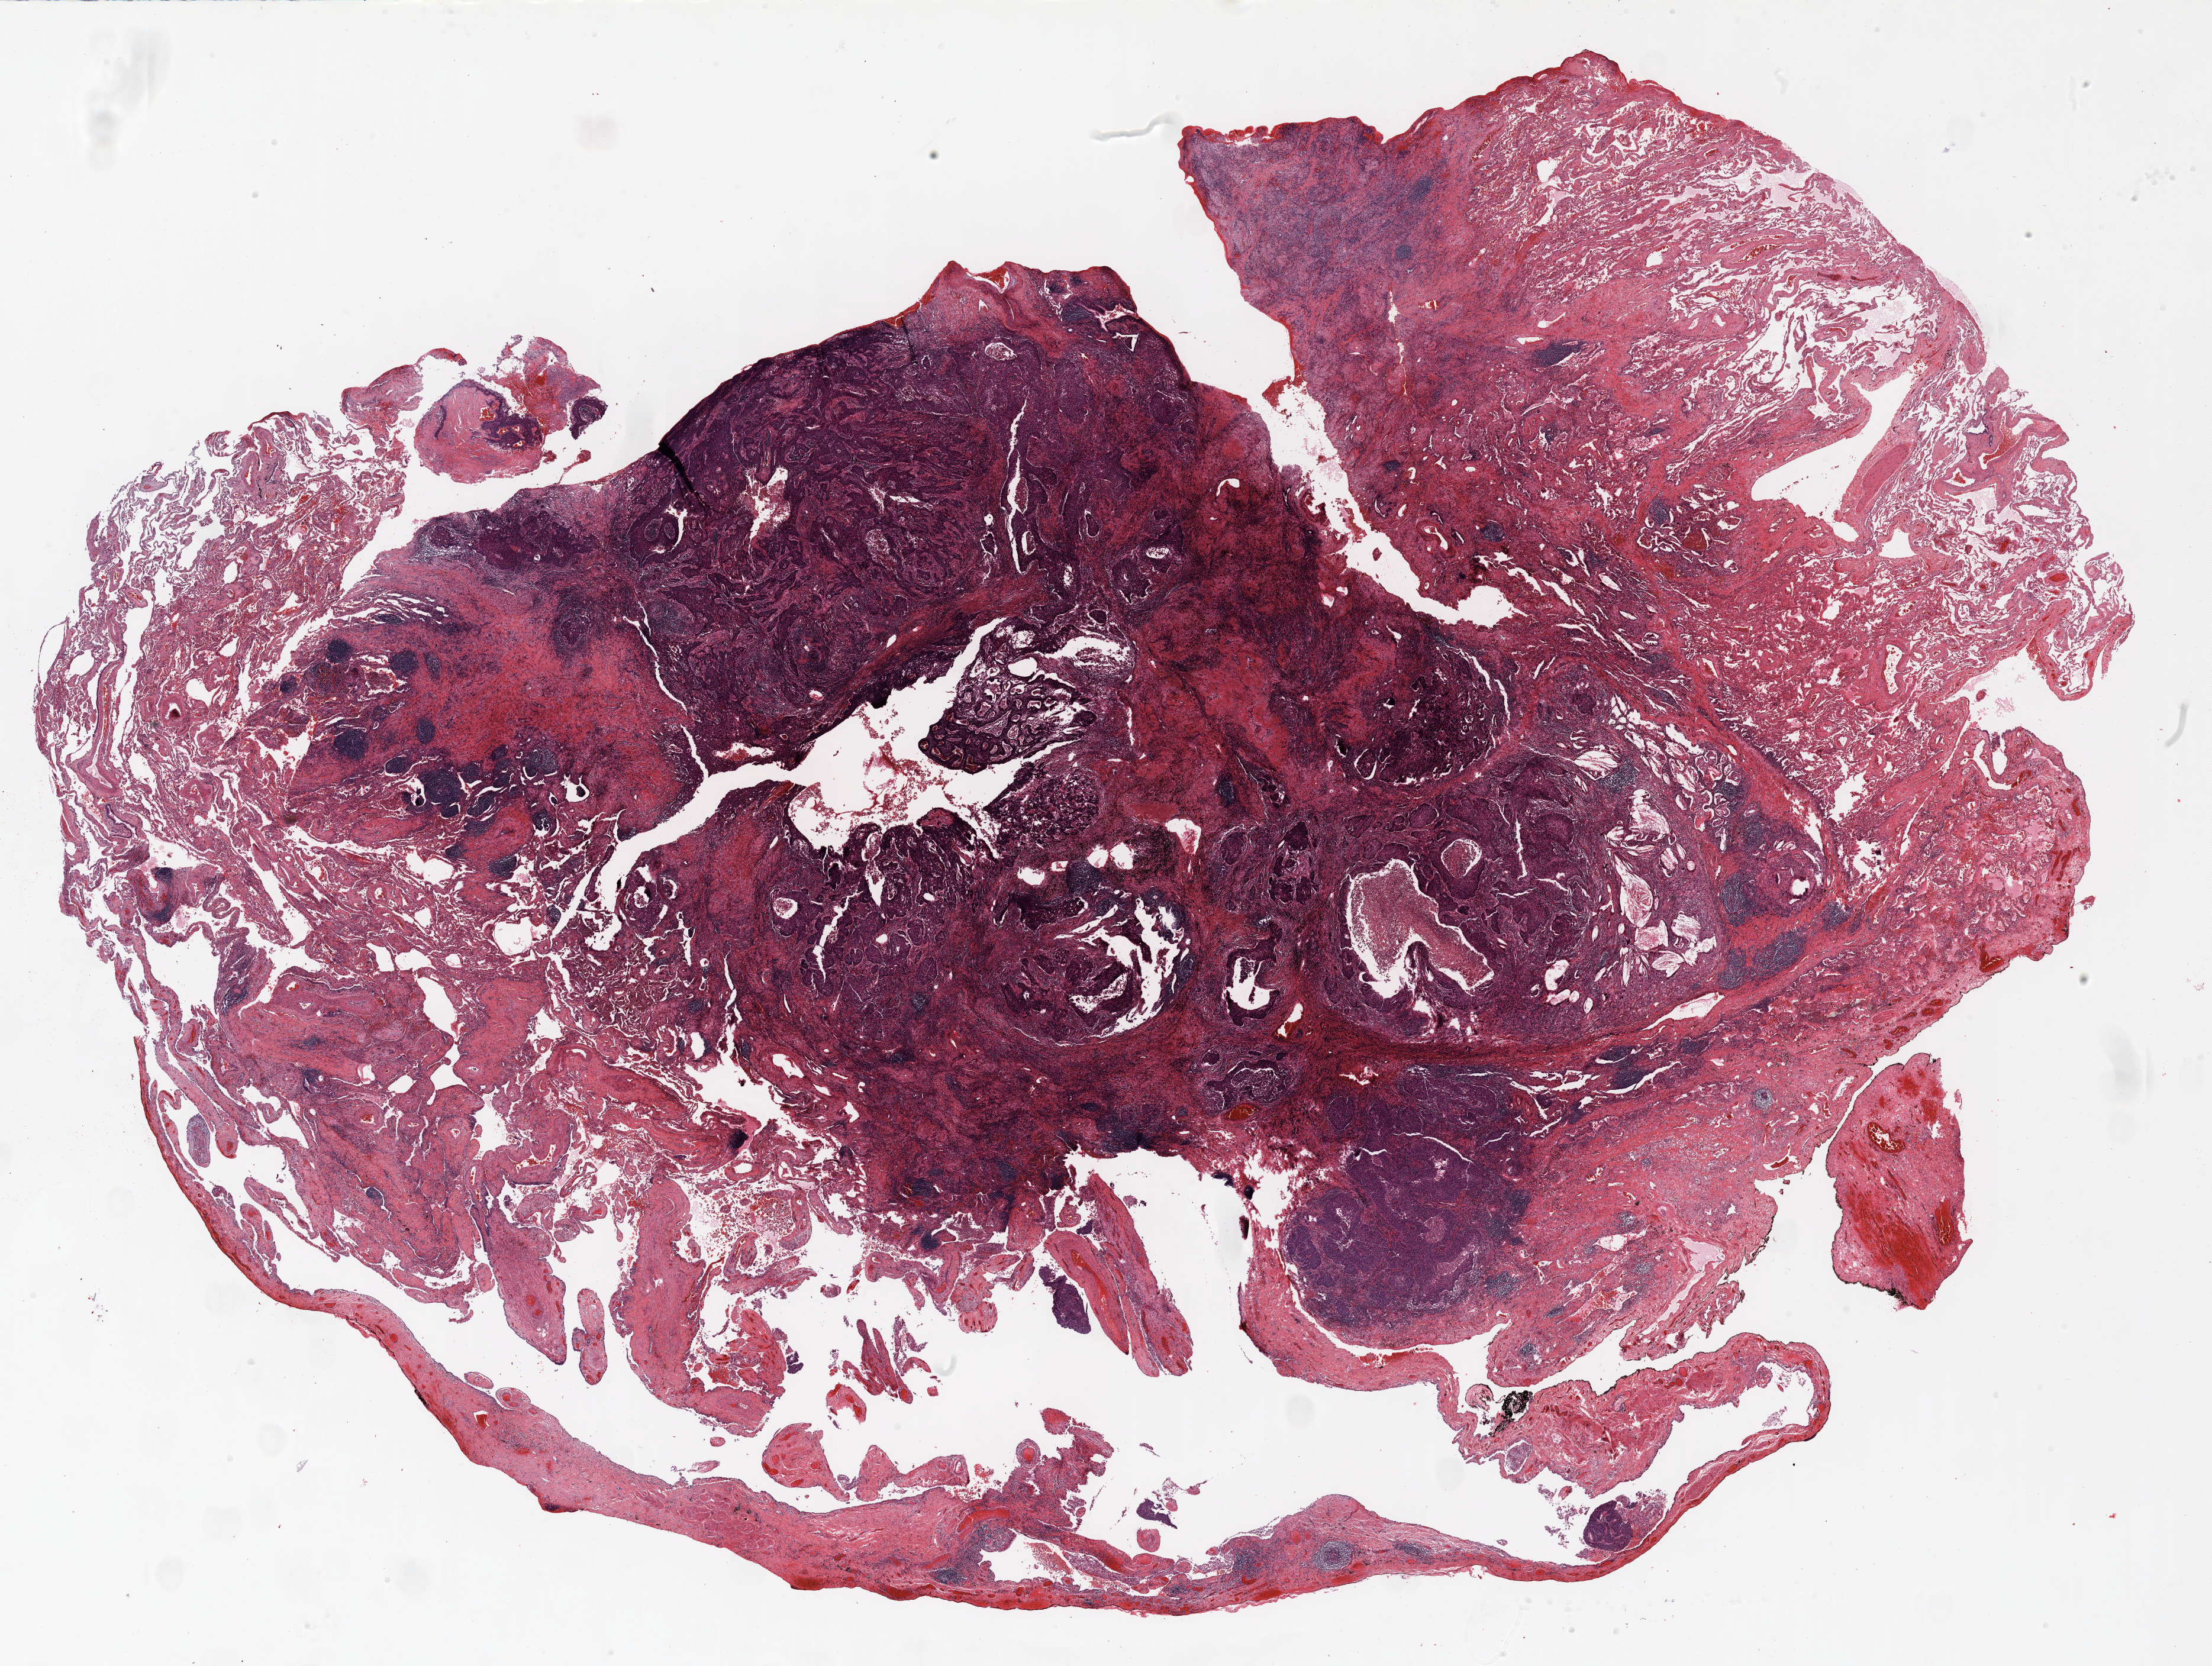
Whole-slide histology image, H&E, low-resolution overview of the scanned area, about 30.0 x 22.6 mm (from a 20x scan). FFPE section. Lung tissue. Male patient, aged 66 at enrolment. Current smoker at enrolment. Grade: poorly differentiated (G3).
Tumour size (pathology): 23 mm. Stage (AJCC 6th edition): IB. ICD-O-3 topography: upper lobe of lung (C34.1). Participant's lung-cancer diagnosis: Squamous cell carcinoma, NOS. Primary tumour location (clinical record): right upper lobe. Note: participant had 2 primary lung cancers recorded; fields above describe the first.